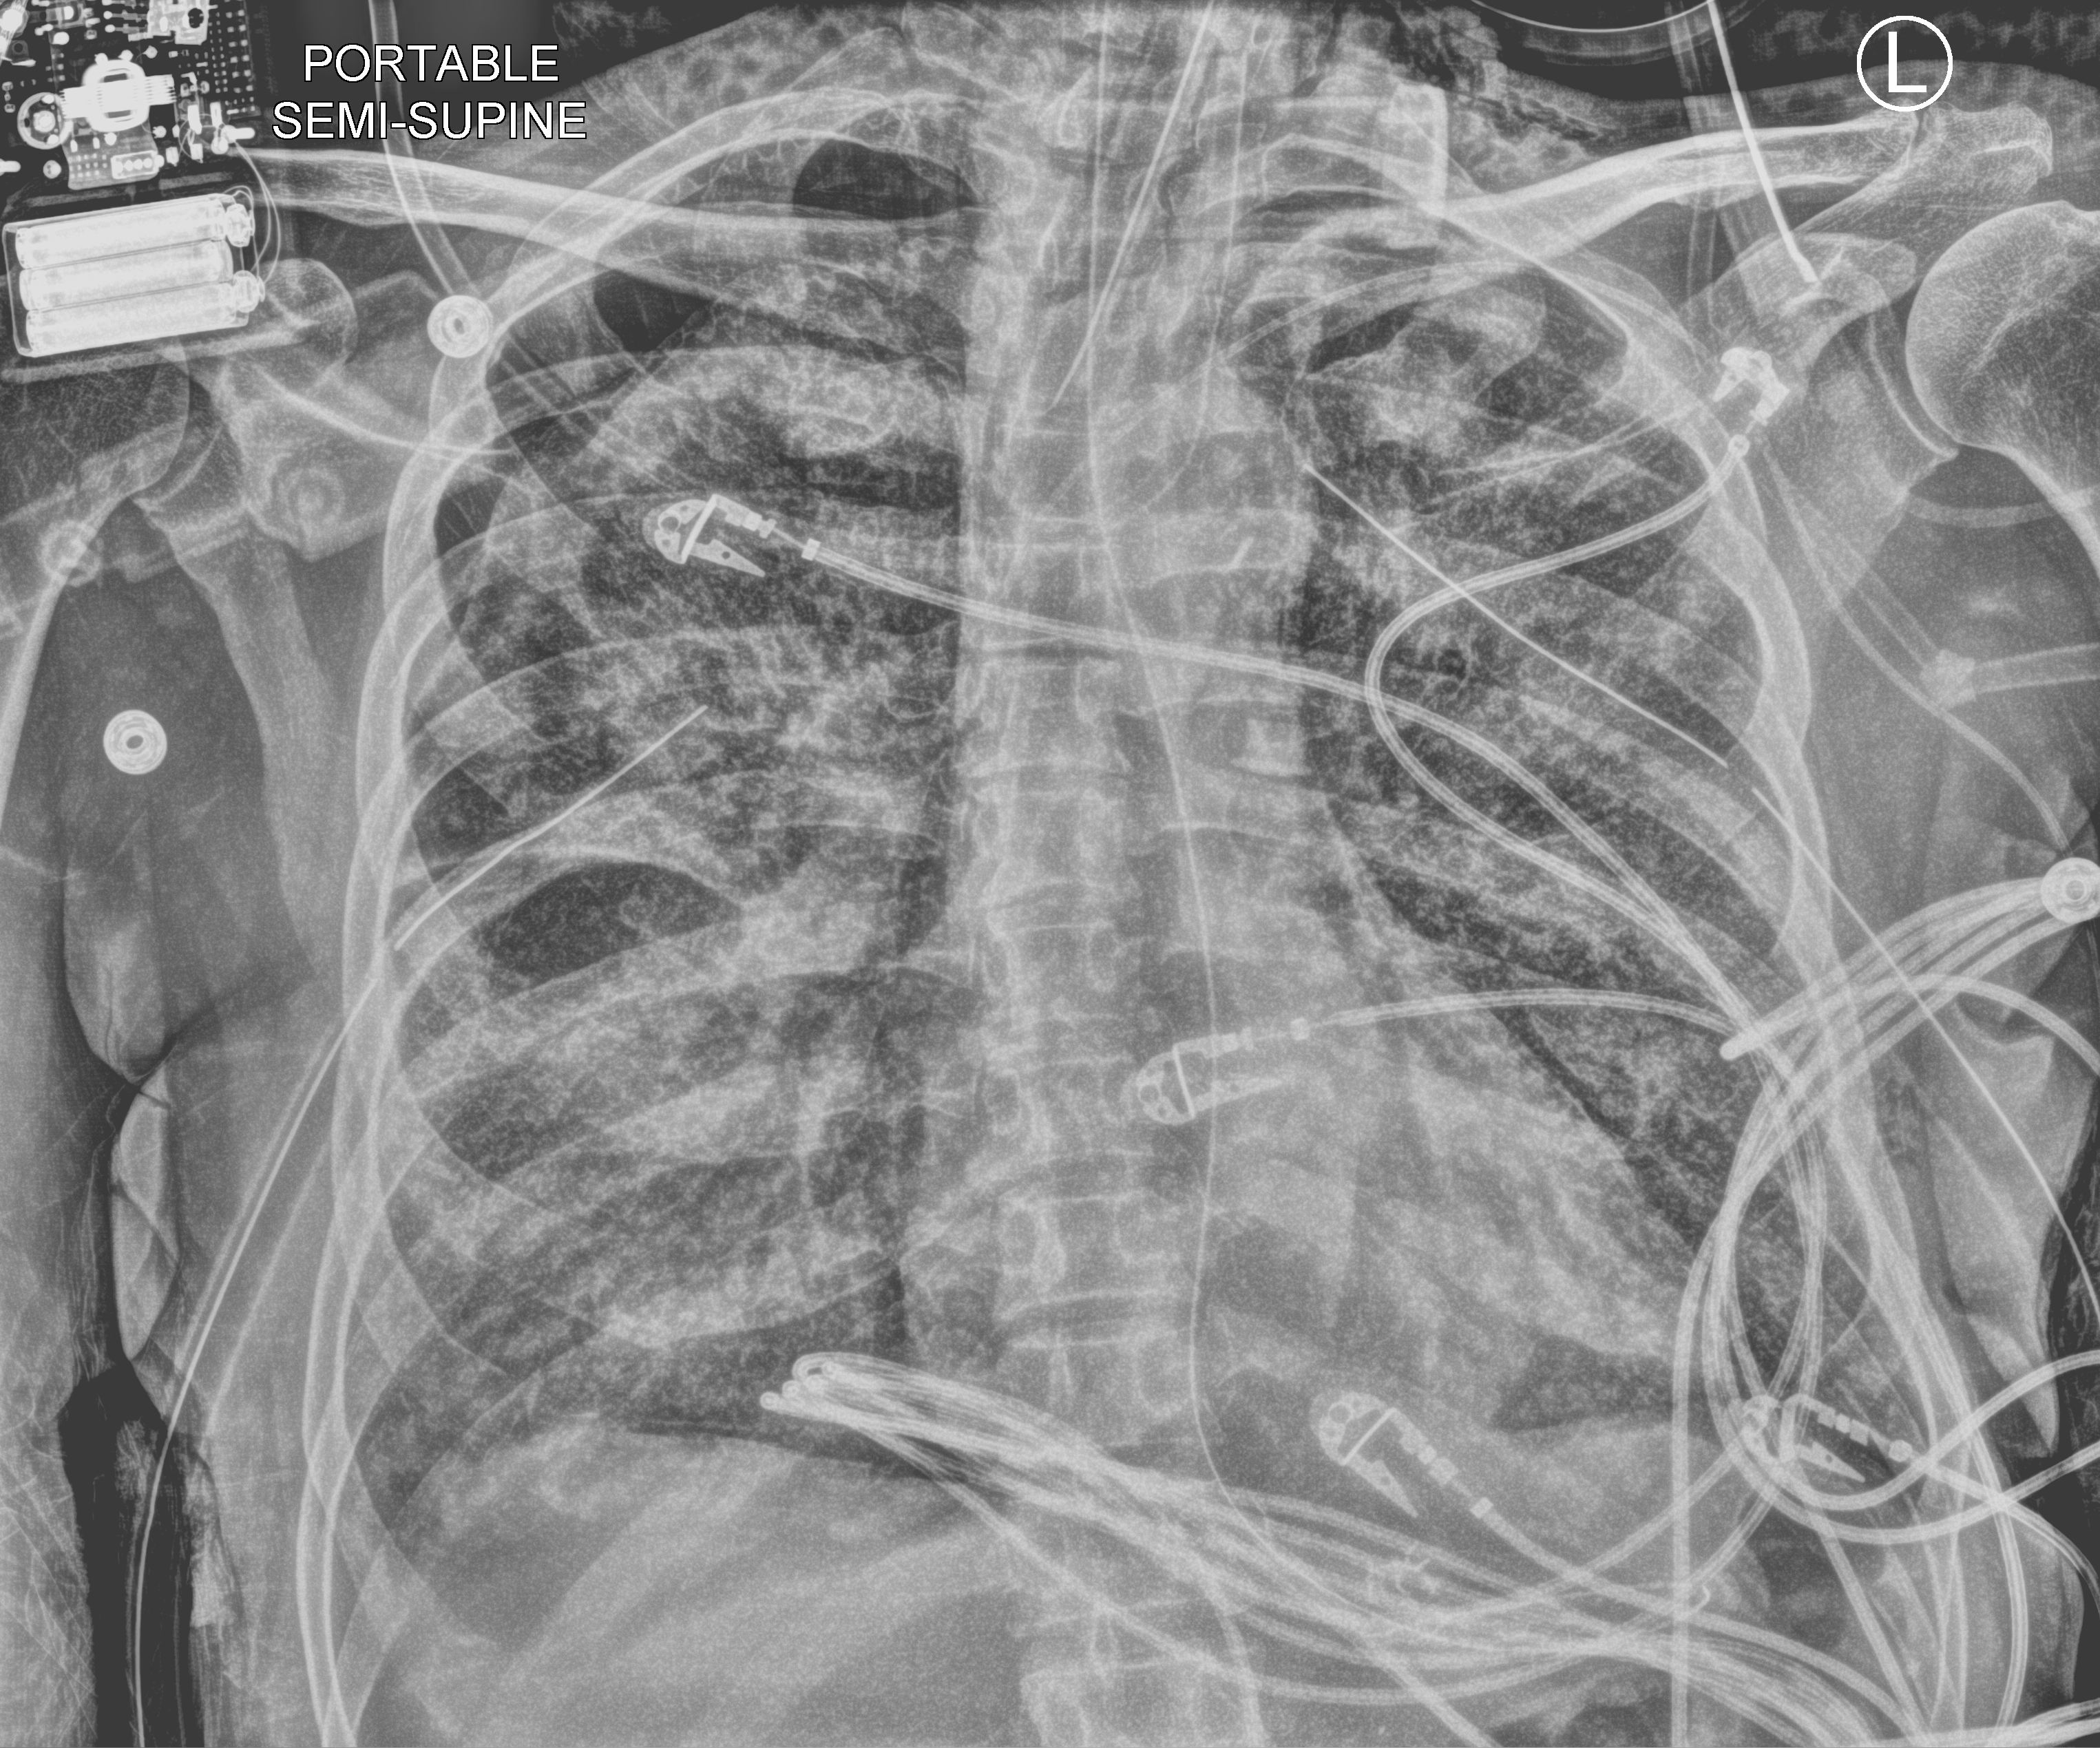
Portable chest radiograph, anteroposterior (AP) projection. Patient hospitalised with COVID-19; male, aged 60–74 years.
Hospital-stay facts (about this admission, not read from this image; timing relative to this image not recorded): chronic kidney disease (admission record): no; admitted to intensive care during this hospital stay: yes; COPD (admission record): no.